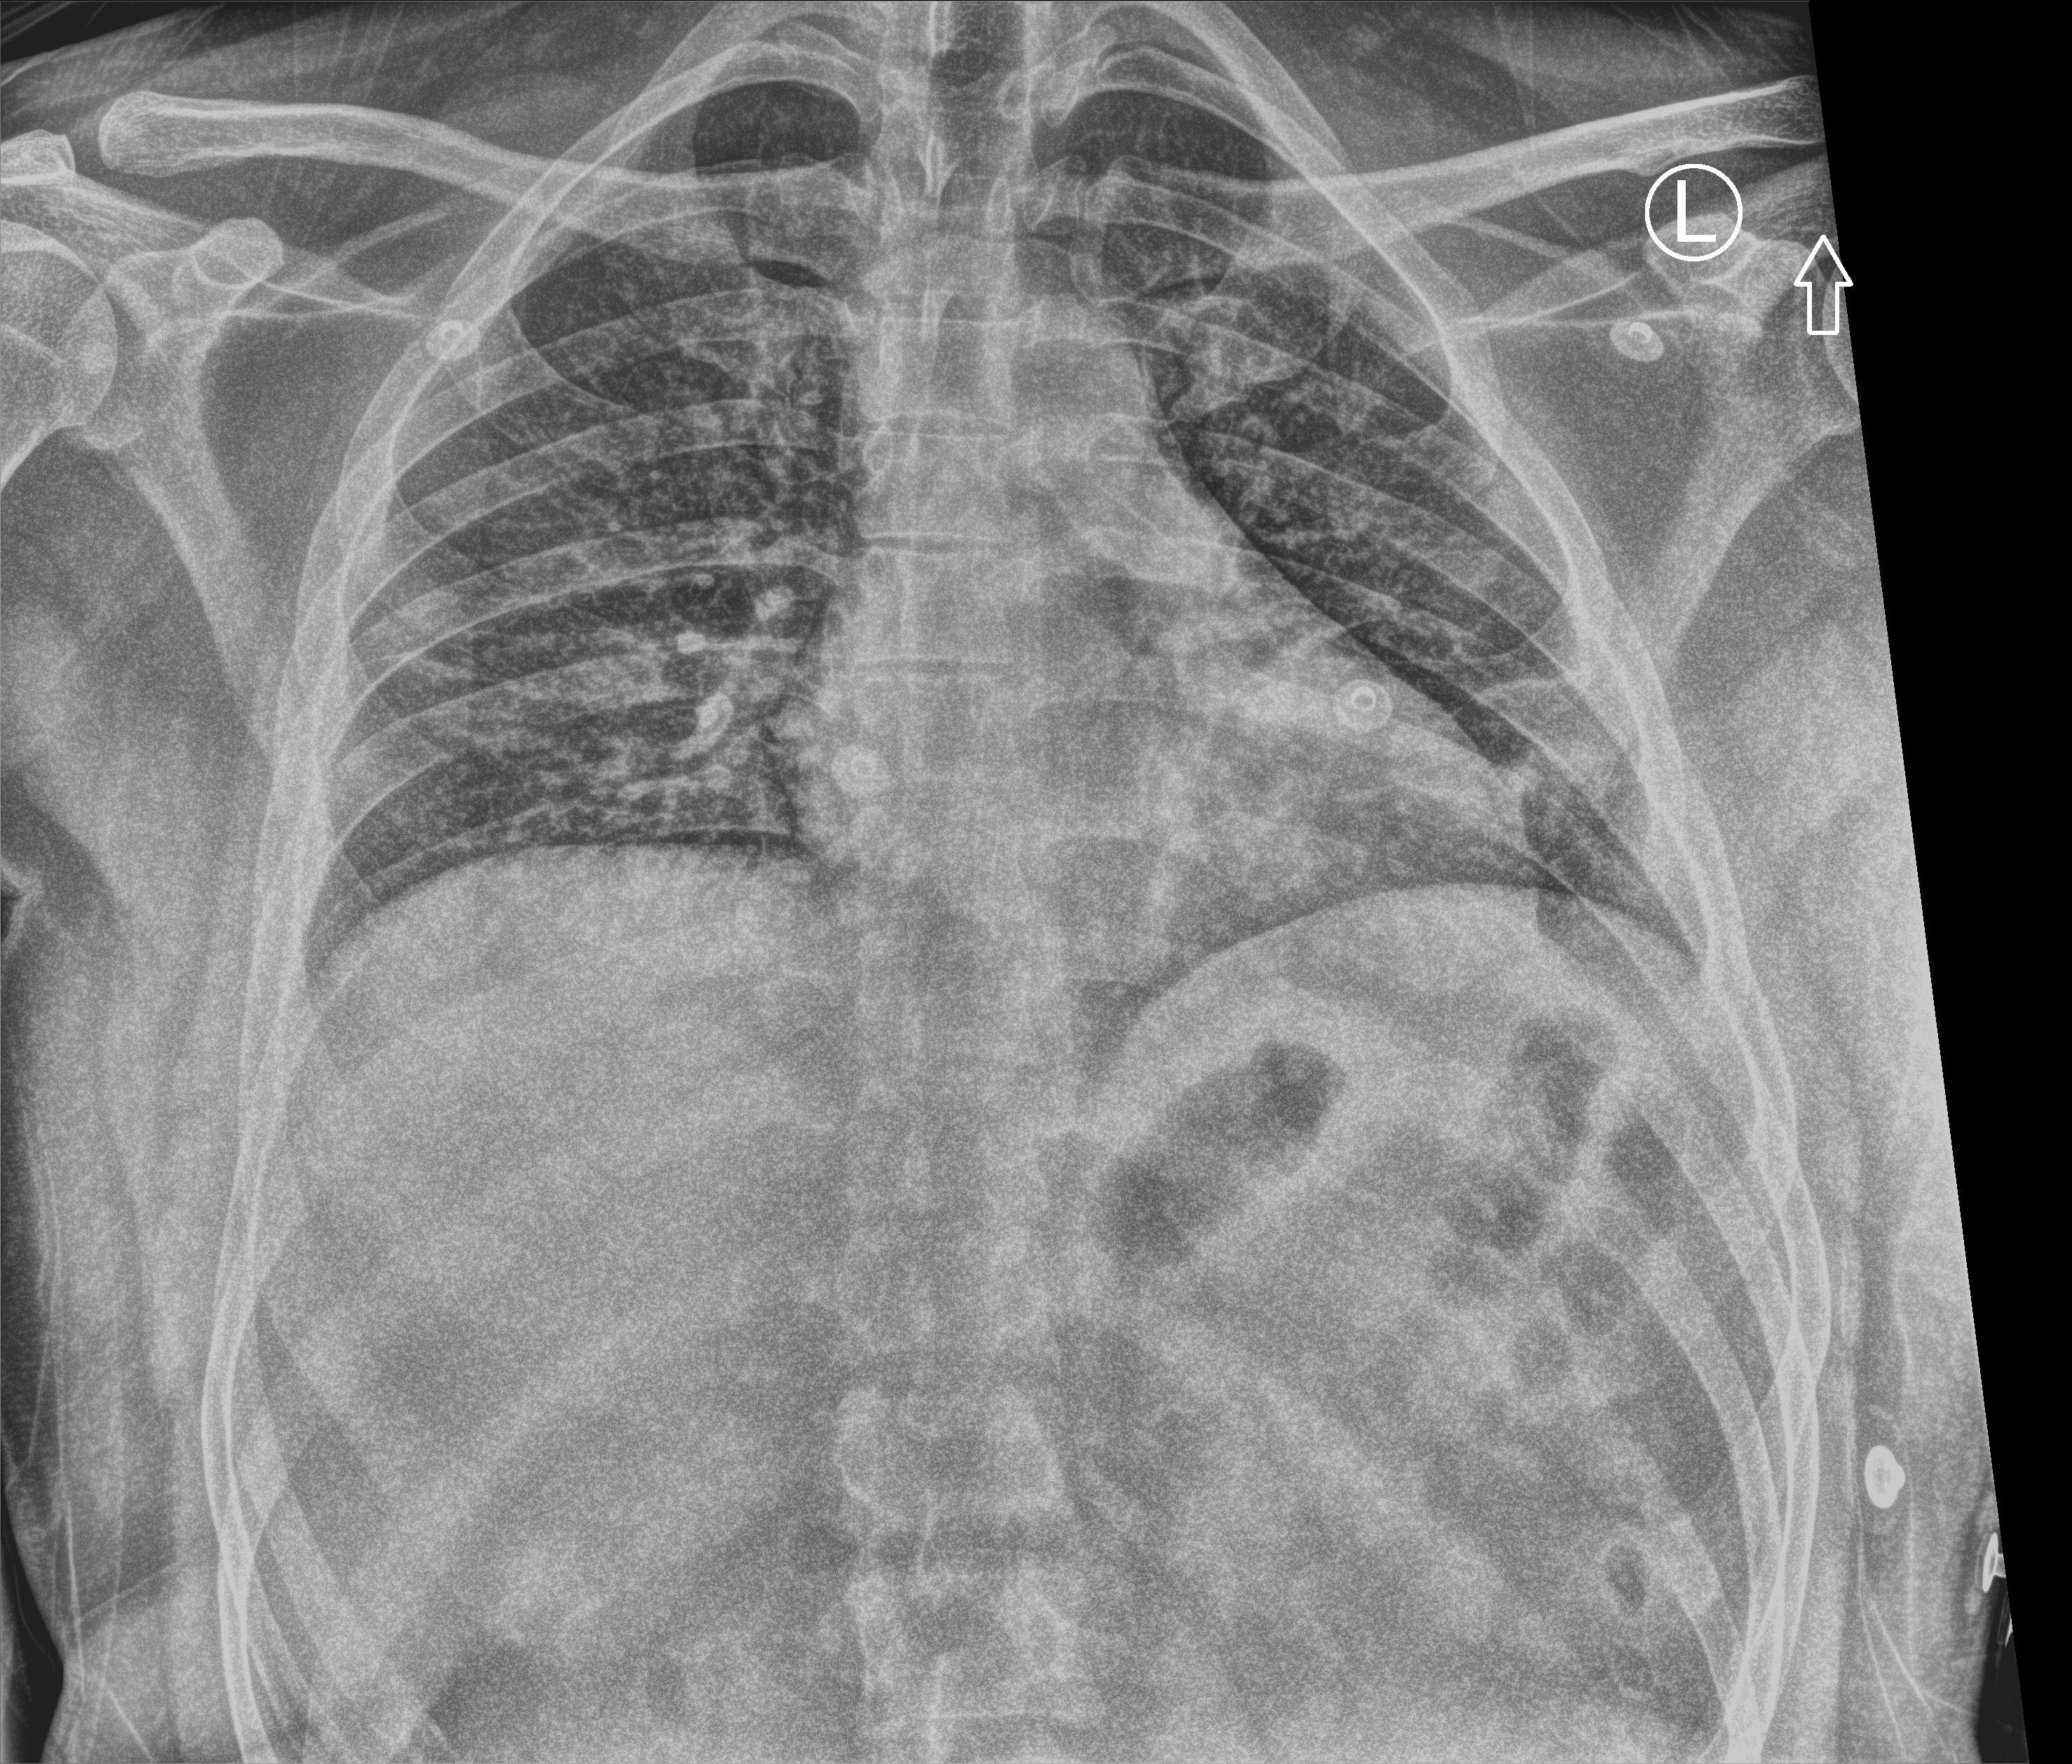
Portable chest radiograph, anteroposterior (AP) projection. Male patient hospitalised with COVID-19, age 18–59 years.
From the hospital-stay record, not from the radiograph (when in the stay this image was taken is not recorded): mechanically ventilated during this hospital stay: no.